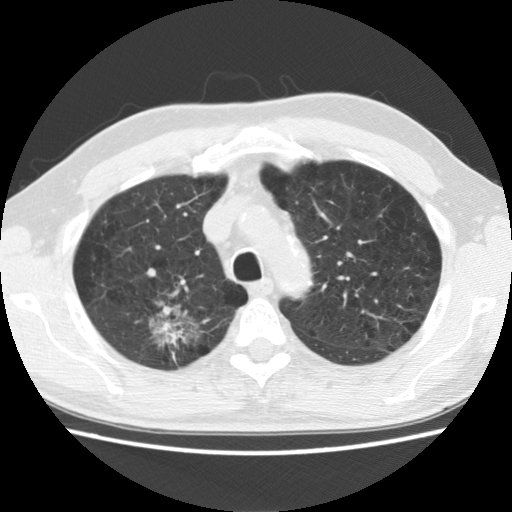
Axial slice from a low-dose chest CT screening exam; baseline annual screen; lung window (W 1500 / L -600 HU); 2.5 mm slice thickness; standard (soft-tissue) reconstruction kernel (STANDARD); slice 38 of 142 in the series. Male participant, aged 64 years at enrolment.
Expert reader's lesion annotation, bounding box <117,296,207,367> (left, top, right, bottom; pixels). Screening reader's record for this exam (one nodule recorded; not confirmed to be the boxed lesion): non-calcified nodule or mass ≥4 mm, right upper lobe, 39 × 31 mm, spiculated (stellate) margins, mixed attenuation.